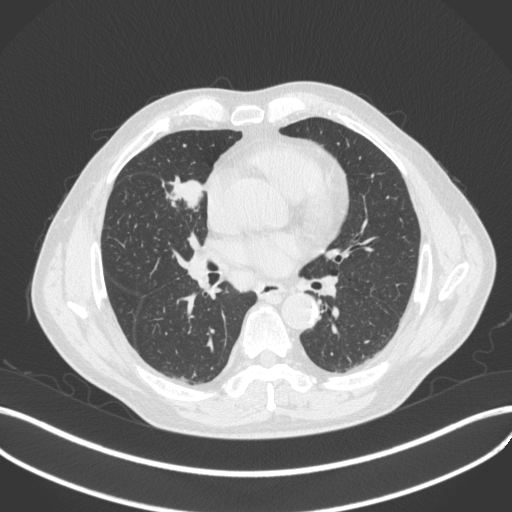
Chest CT, one axial slice; position 201 of 429 along the scan axis; reconstruction kernel B31f; 120 kVp; lung window (W 1500 / L -600 HU); 1 mm slice thickness; 512 × 512 image matrix, field of view 400 × 400 mm. Male patient, age 61 years. From the clinical record (not read from this slice): clinical TNM (as recorded): T2b N1 M0.
Annotated regions visible in this slice (bounding box drawn by a radiologist):
- lung tumour (recorded histology: squamous cell carcinoma): box from (x=159, y=170) to (x=206, y=209) px